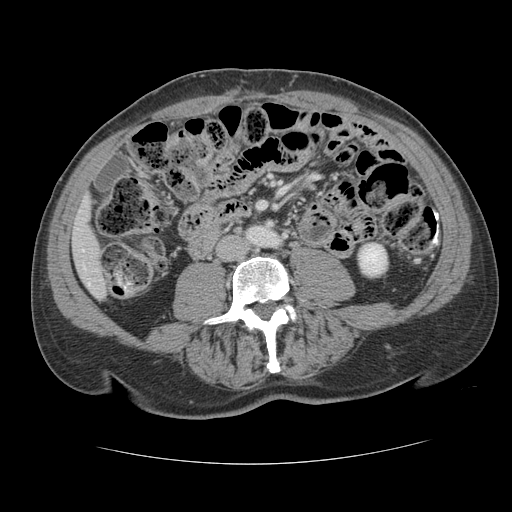
Contrast-enhanced abdominal CT, one axial slice; reconstruction kernel STANDARD; 120 kVp; intravenous contrast given; soft-tissue window (W 400 / L 40 HU); 2.5 mm slice thickness; 512 × 512 image matrix. Male patient, age 68 years. Case-level facts recorded for this patient, not image findings: diagnosis: colorectal cancer liver metastases, imaged before liver resection; multiple liver metastases: yes; largest metastasis: 2.2 cm.
Structures marked on this image (expert manual segmentation):
- liver: box from (x=73, y=203) to (x=107, y=297) px
- planned liver remnant (the part of the liver to remain after resection): (x=73, y=204)–(x=107, y=297)
- portal vein (with intrahepatic branches): (x=88, y=283)–(x=90, y=285)